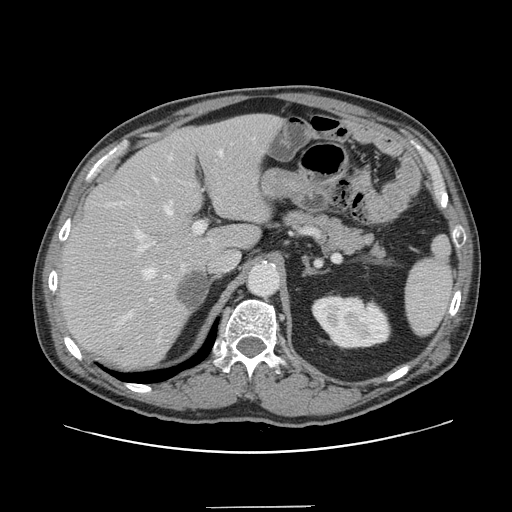
Contrast-enhanced abdominal CT, one axial slice; position 97 of 139 along the scan axis; 120 kVp; intravenous contrast given; soft-tissue window (W 400 / L 40 HU); 2.5 mm slice thickness; 512 × 512 image matrix. Male patient, age 64 years. From the clinical record (not read from this slice): diagnosis: colorectal cancer liver metastases, imaged before liver resection; multiple liver metastases: yes; largest metastasis: 3.5 cm; disease in both lobes: yes.
Outlined on this slice (outlined manually by an expert reader):
- hepatic veins: bounding box (x1, y1, x2, y2) in pixels: (121, 149, 223, 321)
- liver: (61, 115, 280, 367)
- planned liver remnant (the part of the liver to remain after resection): (61, 116, 269, 366)
- portal vein (with intrahepatic branches): (132, 221, 205, 271)
- liver metastasis: (177, 270, 206, 311)